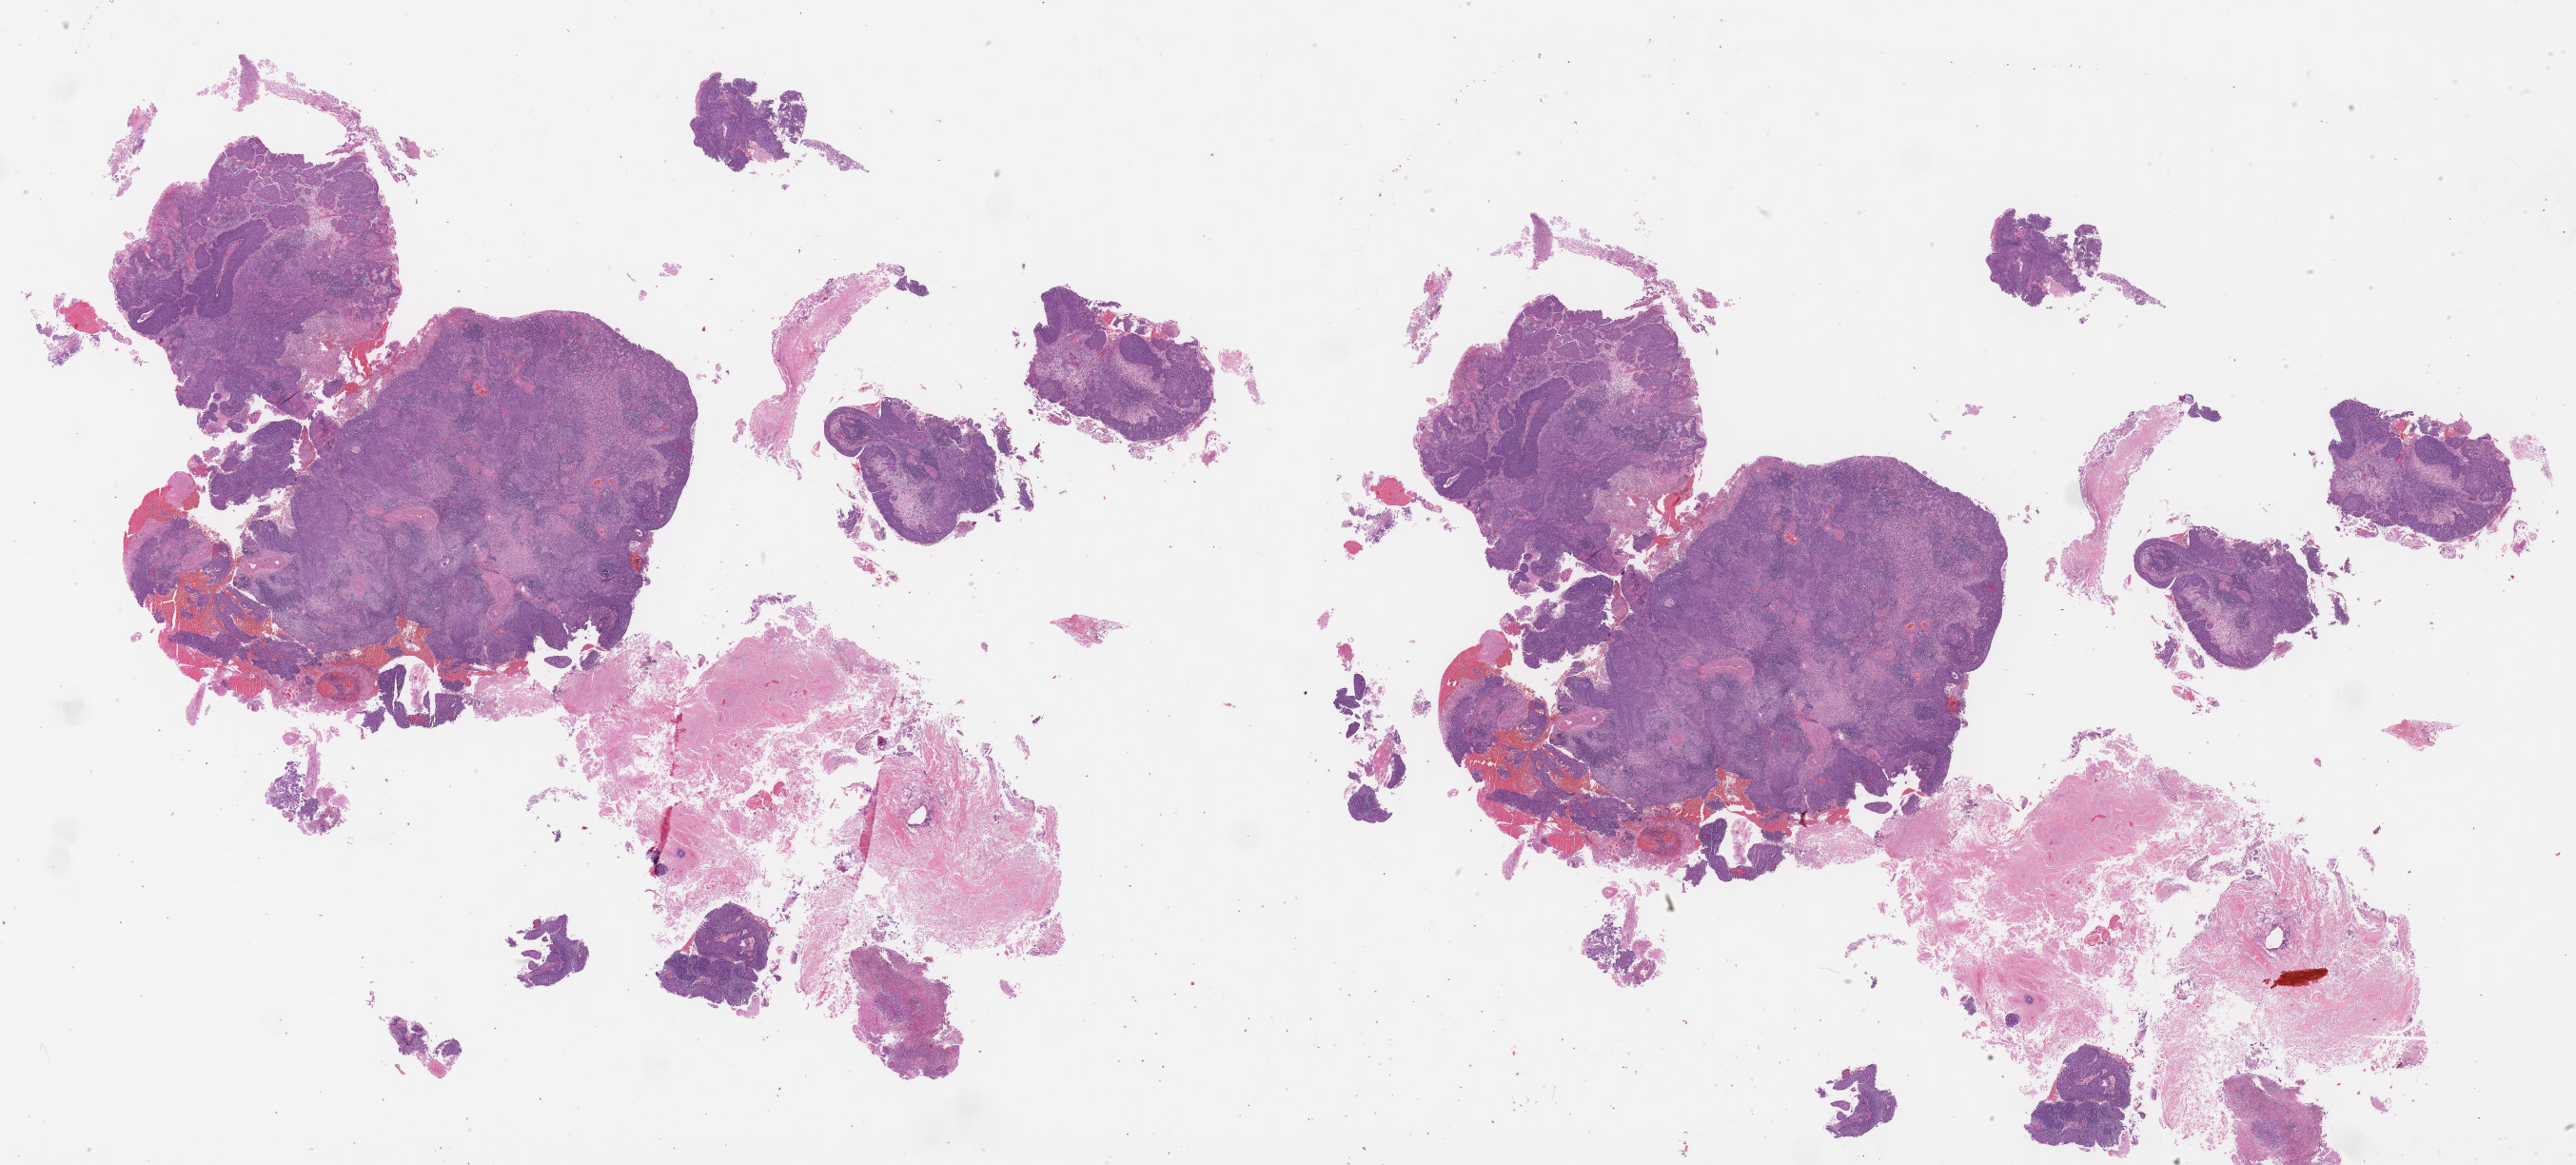
H&E whole-slide image — a low-resolution overview of the entire scanned area, about 43.8 x 19.8 mm; FFPE section; cervix, primary tumour sample. Female patient; age at initial diagnosis 33 years. Histologic grade: G2 (moderately differentiated).
Pathologic diagnosis: Squamous cell carcinoma, NOS (cervix uteri). FIGO stage: IIB.